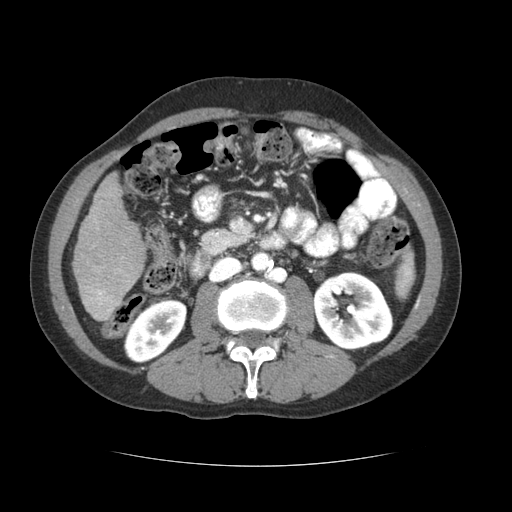
Contrast-enhanced abdominal CT (liver protocol), one axial slice; slice 18 of 69 in the series (ordered by position); reconstruction kernel STANDARD; soft-tissue window (W 400 / L 40 HU); 2.5 mm slice thickness; 512 × 512 image matrix. From the clinical record (not read from this slice): diagnosis: hepatocellular carcinoma (patient treated with transarterial chemoembolisation; whether this scan precedes or follows treatment is not stated here); TNM stage (as recorded): Stage-II; Child-Pugh class: B; tumour differentiation: poorly differentiated; tumour size: 2.6 cm.
Structures marked on this image (semi-automatic segmentation, software-assisted and operator-edited):
- liver parenchyma outside the tumour (the mass and vessels are separate outlines, so this box may not span the whole liver): bounding box <72,173,146,320> (left, top, right, bottom; pixels)
- liver vessels: <88,269,121,317>